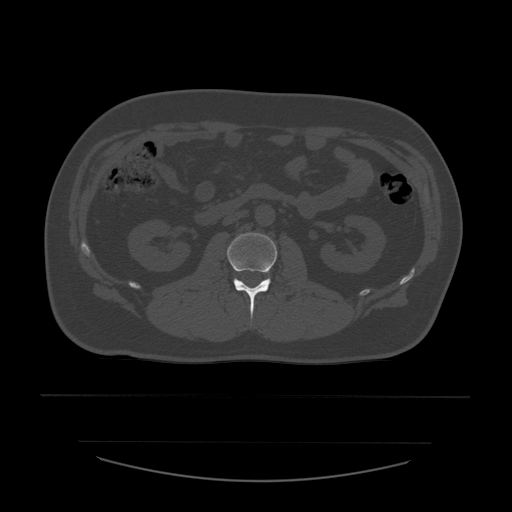
CT including the spine, one axial slice. Slice 198 of 532 in the series (ordered by position). 120 kVp. Bone window (W 1800 / L 400 HU). 1.25 mm slice thickness. 512 × 512 image matrix, field of view 441 × 441 mm. Patient age 44 years. Case-level facts recorded for this patient, not image findings: primary cancer: soft tissue sarcoma.
Structures marked on this image (semi-automatically segmented with operator editing):
- L2 vertebra: box from (x=227, y=233) to (x=278, y=318) px